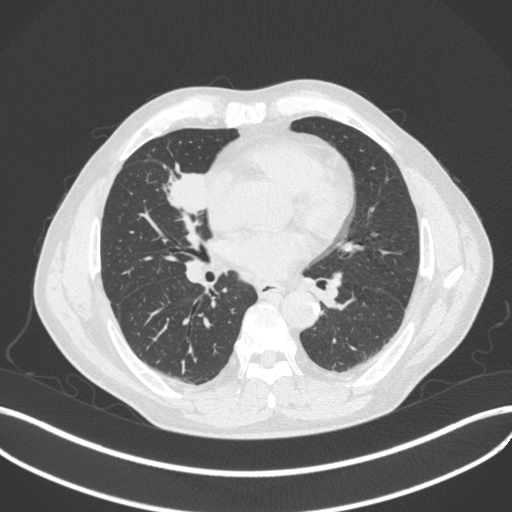
Chest CT, one axial slice. Position 192 of 429 along the scan axis. Reconstruction kernel B31f. 120 kVp. Lung window (W 1500 / L -600 HU). 1 mm slice thickness. 512 × 512 image matrix. Male patient, age 61 years. Case-level facts recorded for this patient, not image findings: clinical TNM (as recorded): T2b N1 M0.
Outlined on this slice (rectangle marked by the reading radiologist):
- lung tumour (recorded histology: squamous cell carcinoma): bounding box <162,161,214,218> (left, top, right, bottom; pixels)